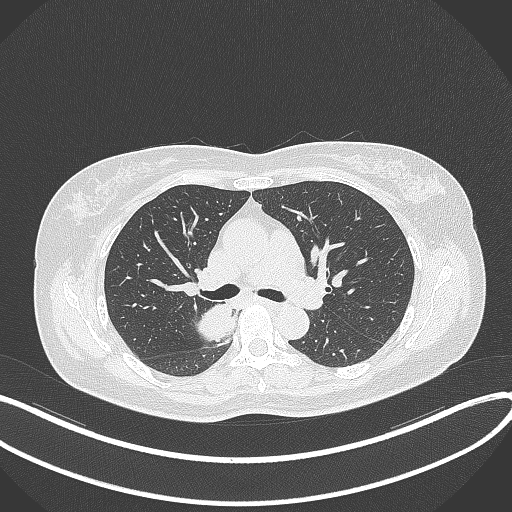
Chest CT, one axial slice. Slice 229 of 331 in the series (ordered by position). Reconstruction kernel B70f. 120 kVp. Lung window (W 1500 / L -600 HU). 1 mm slice thickness. 512 × 512 image matrix. Female patient, age 54 years. Case-level facts recorded for this patient, not image findings: clinical TNM (as recorded): T4 N0 M0.
Structures marked on this image (rectangle marked by the reading radiologist):
- lung tumour (recorded histology: adenocarcinoma): box from (x=190, y=297) to (x=238, y=347) px